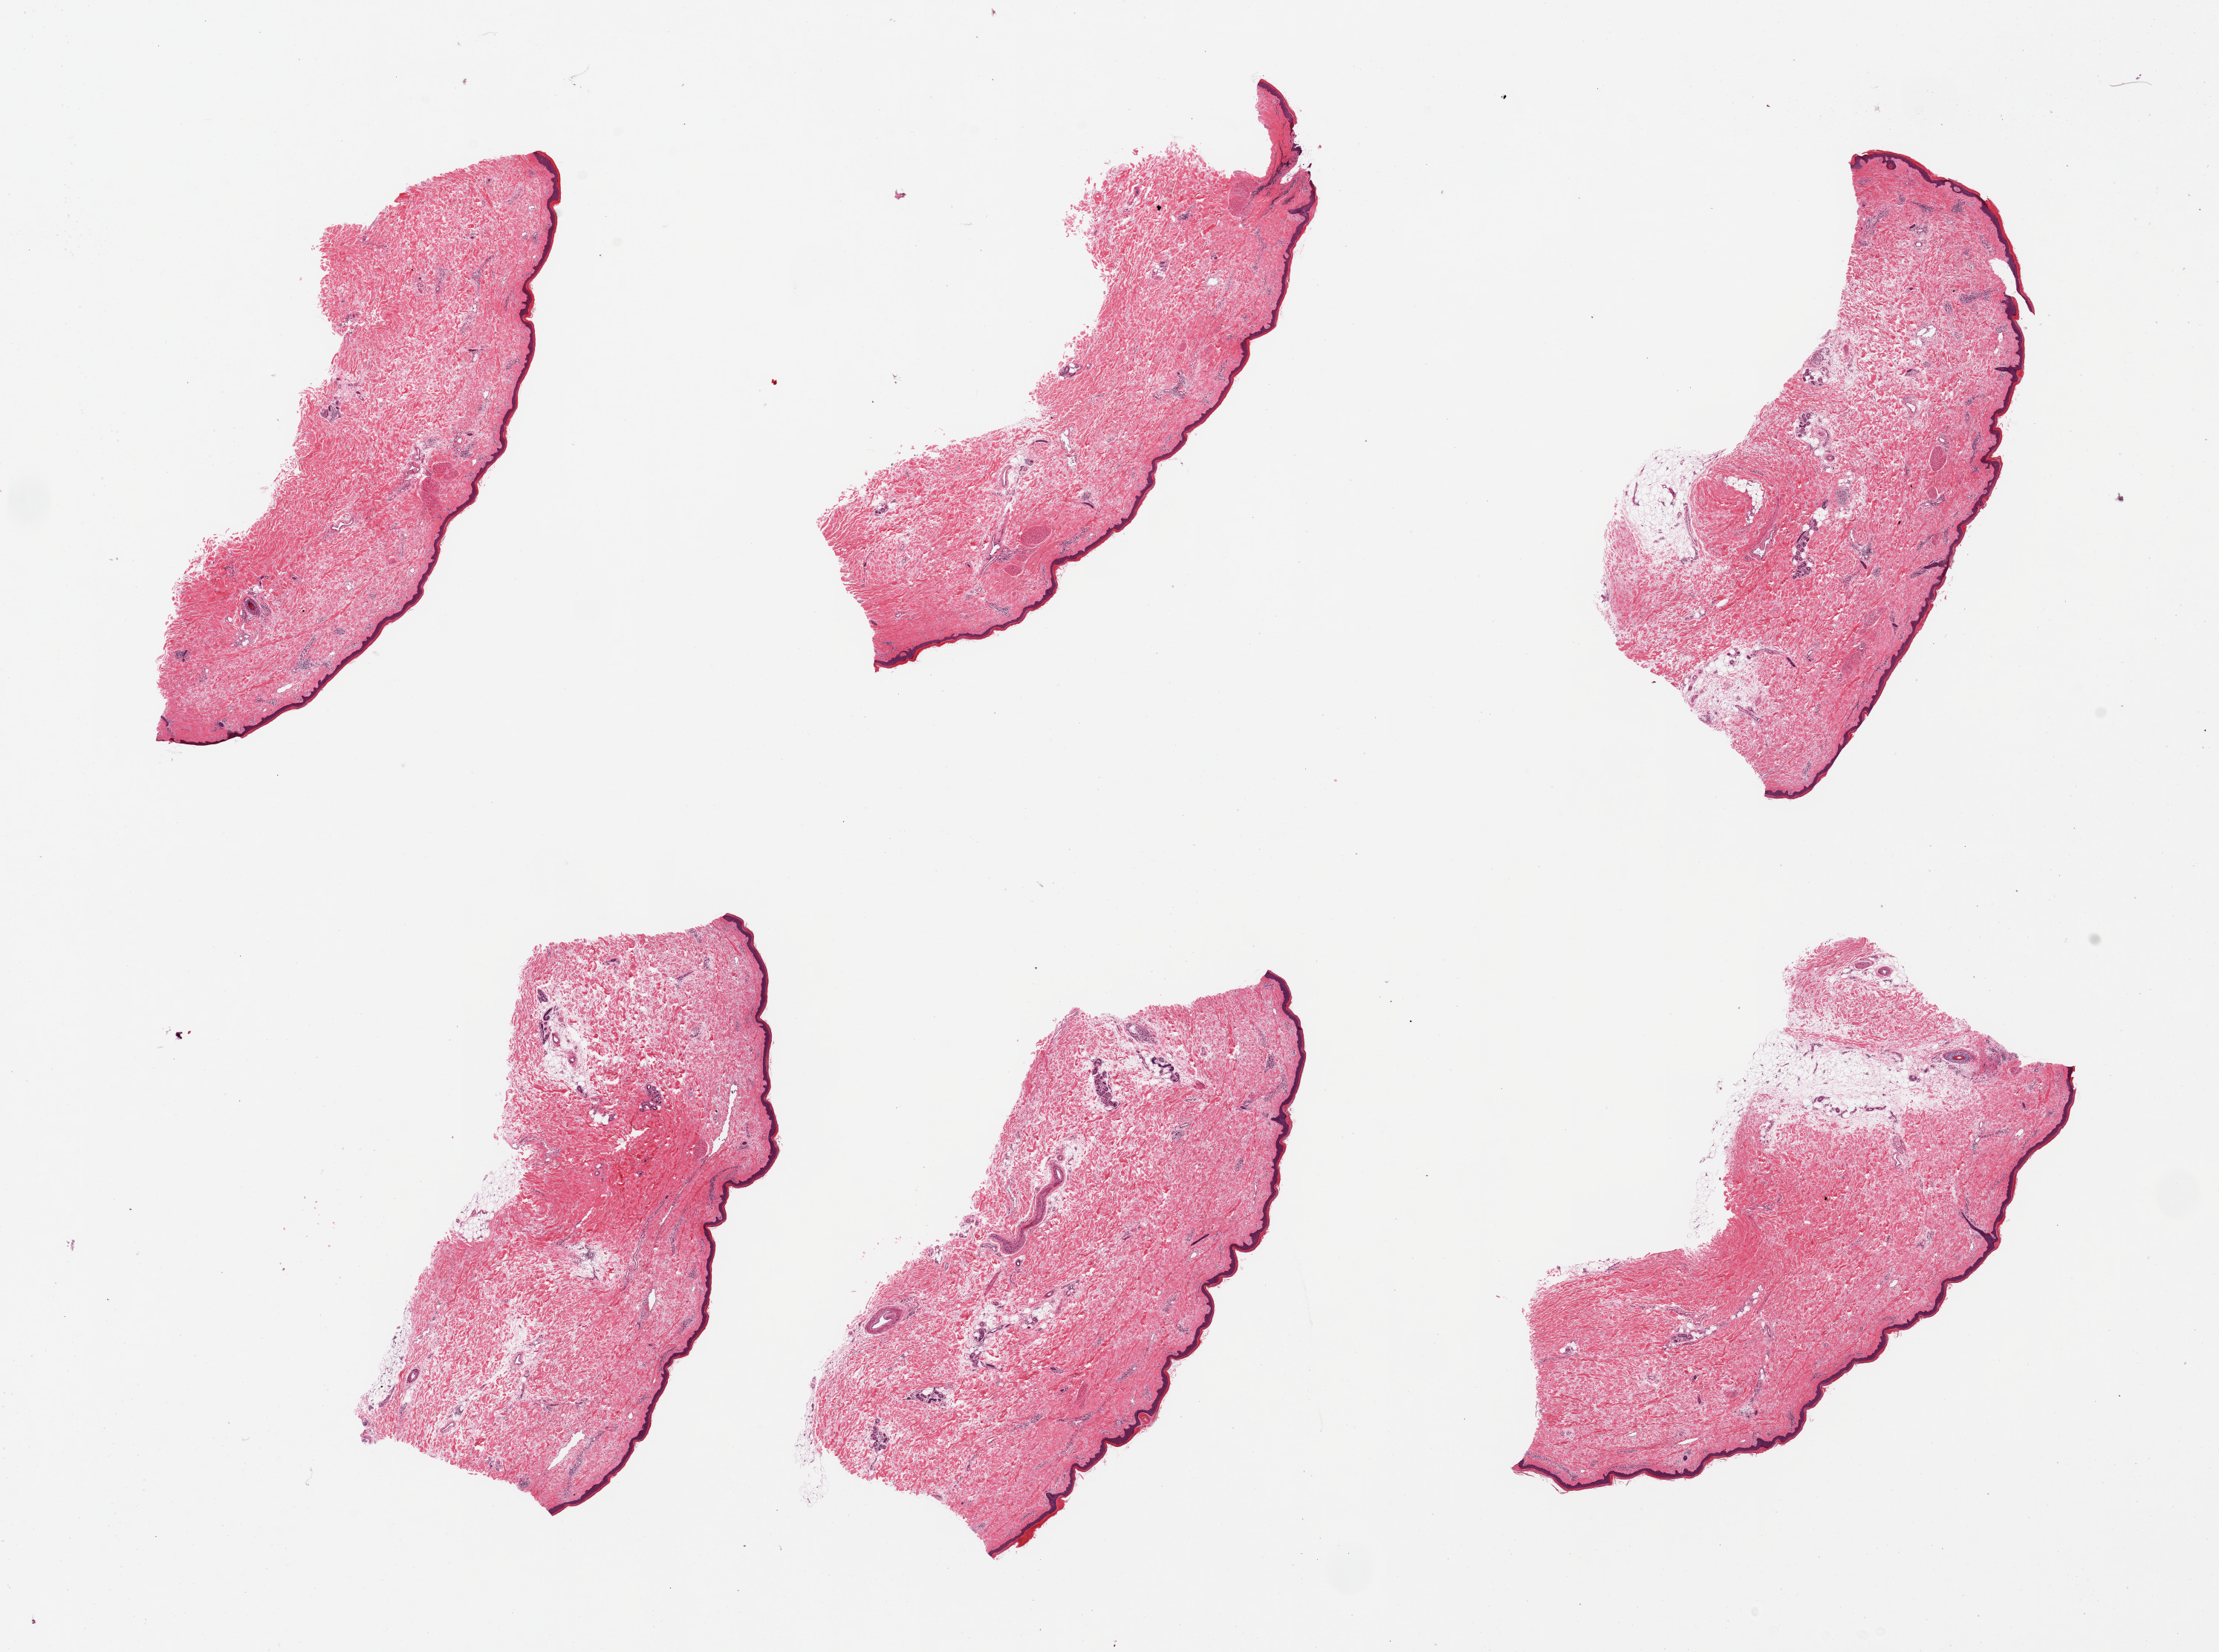
Hematoxylin and eosin (H&E) whole-slide image, brightfield, low-resolution overview of the scanned area, about 23.6 x 17.6 mm. PAXgene-fixed paraffin-embedded (PFPE) section. Section of skin of lower leg (target tissue). Tissue donor sample. Donor: male.
Pathologist's review note for this sample: 6 pieces, well trimmed.